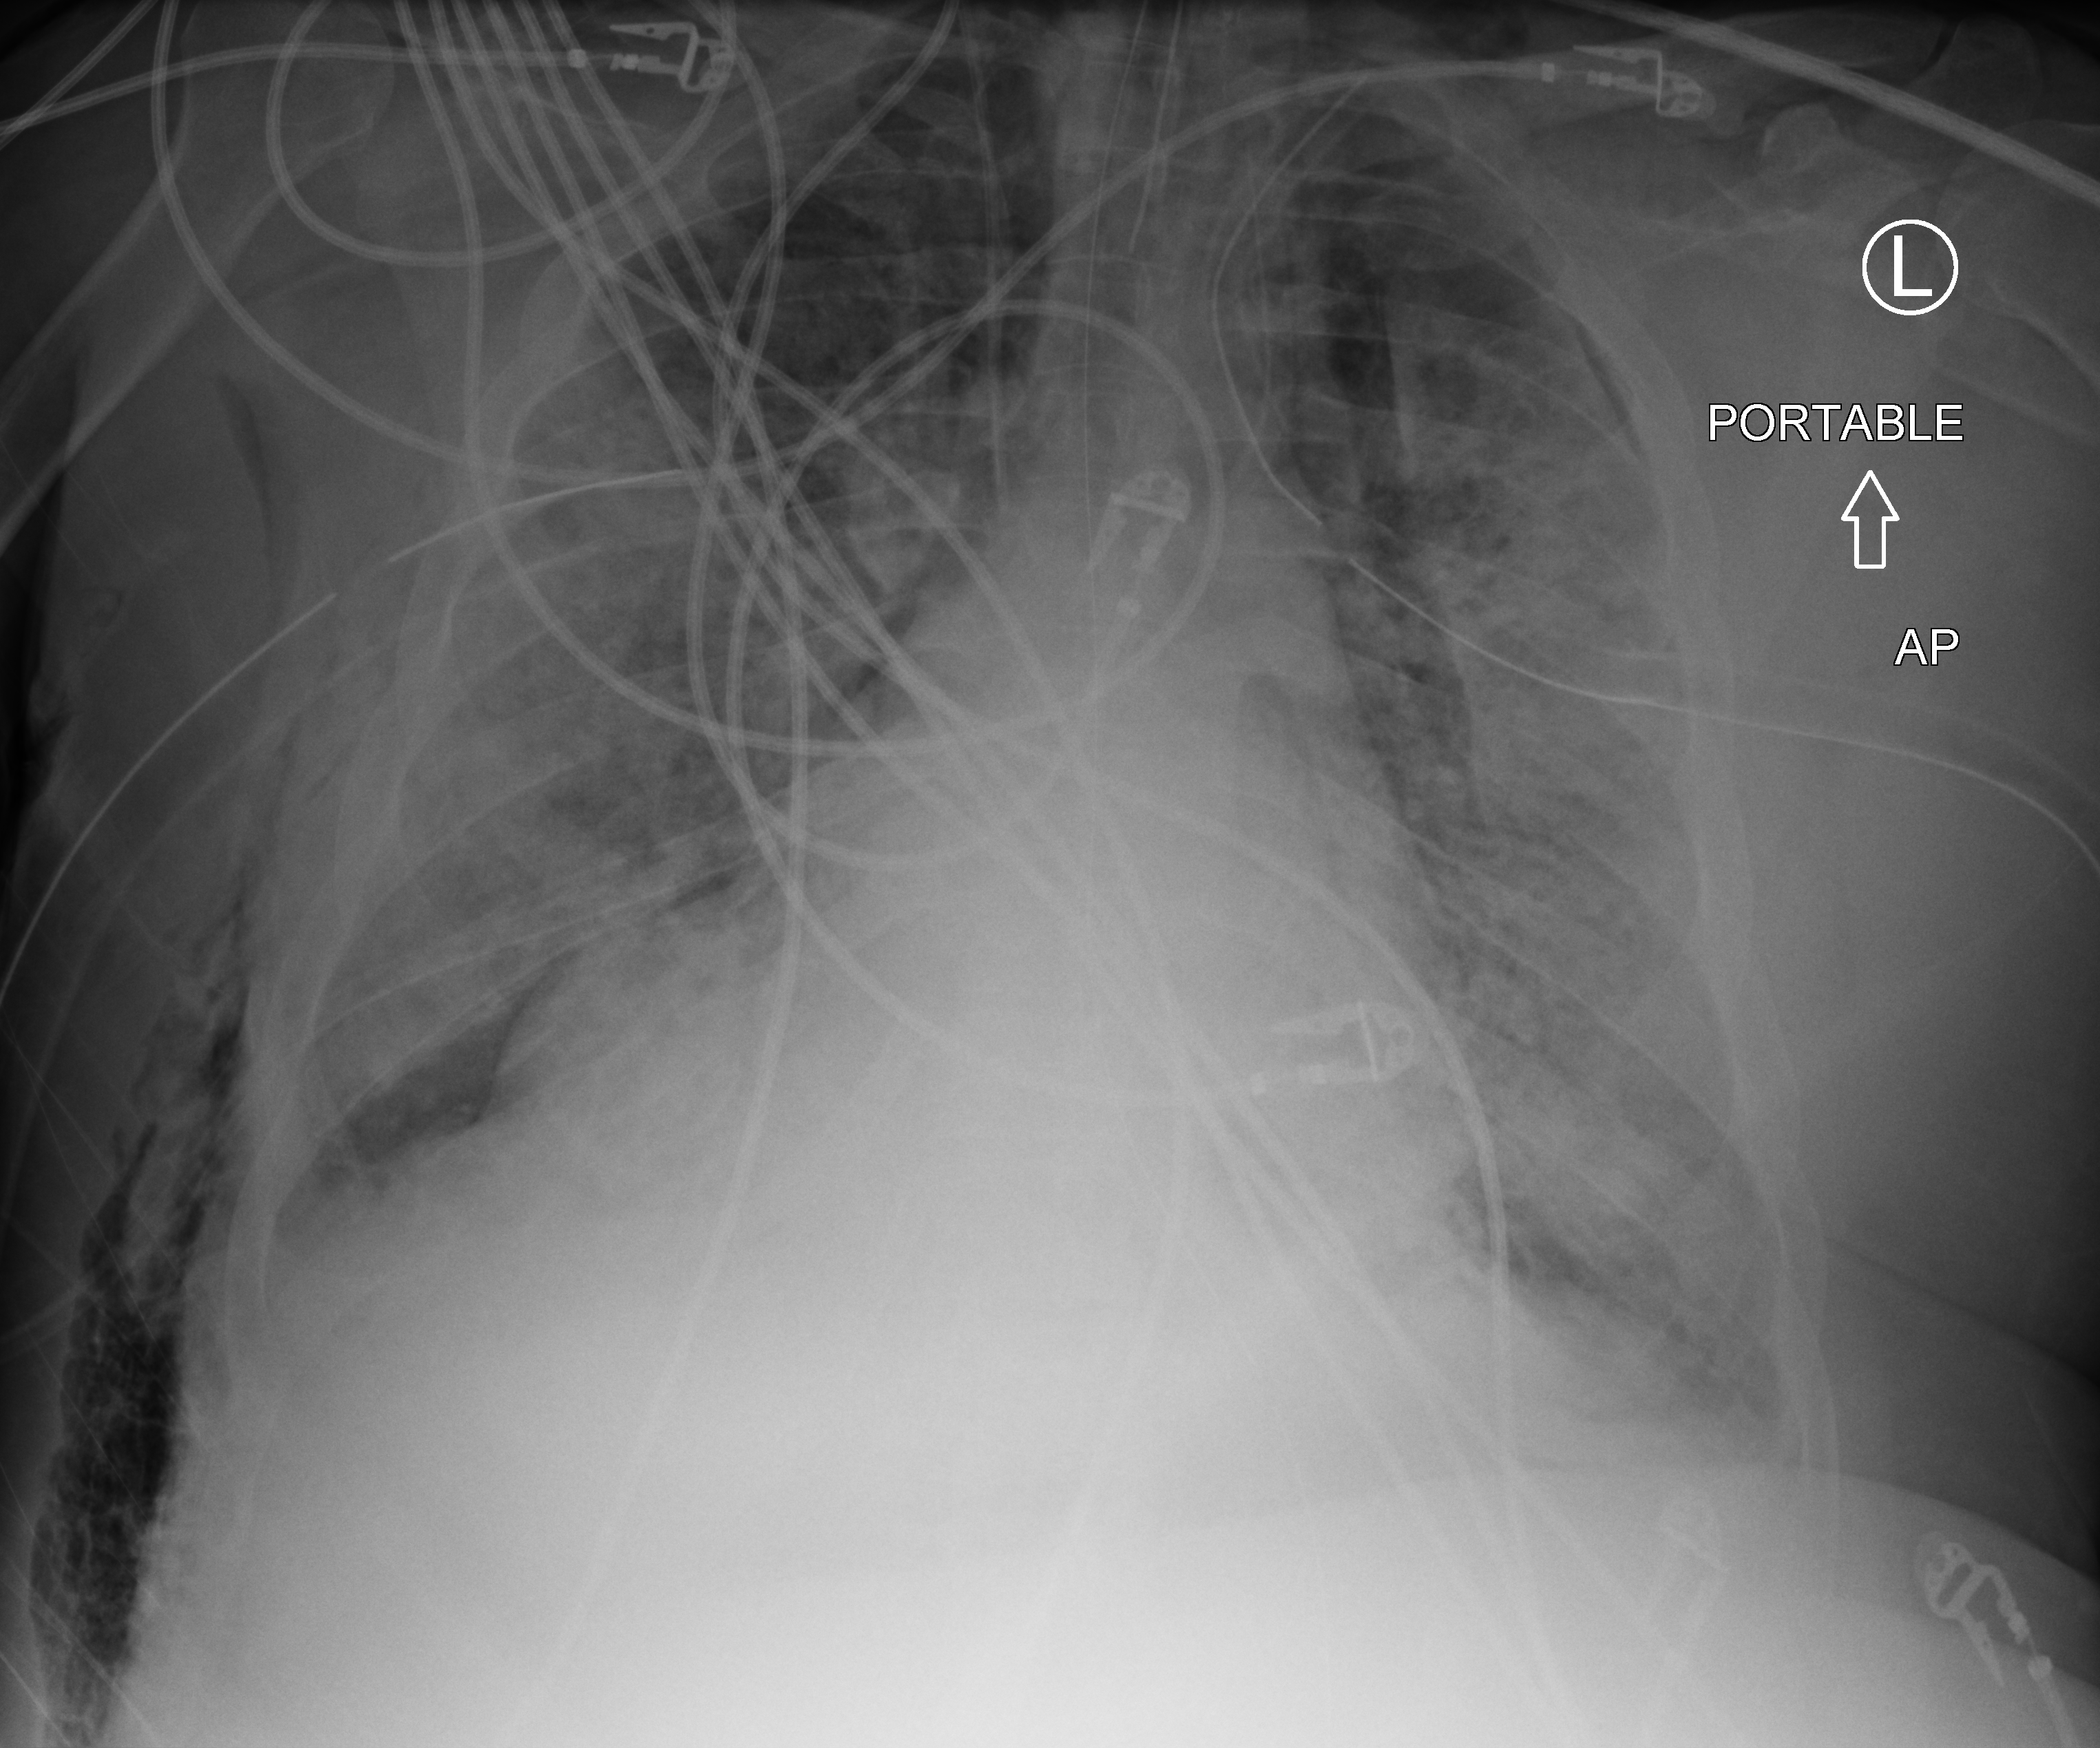
Bedside chest radiograph (computed radiography); anteroposterior (AP) projection. Adult patient hospitalised with COVID-19, age 18–59 years.
Admission-level facts for this patient (not findings on this image; timing relative to this image not recorded):
- mechanically ventilated during this hospital stay: yes
- COPD (admission record): no
- other chronic lung disease (admission record): no